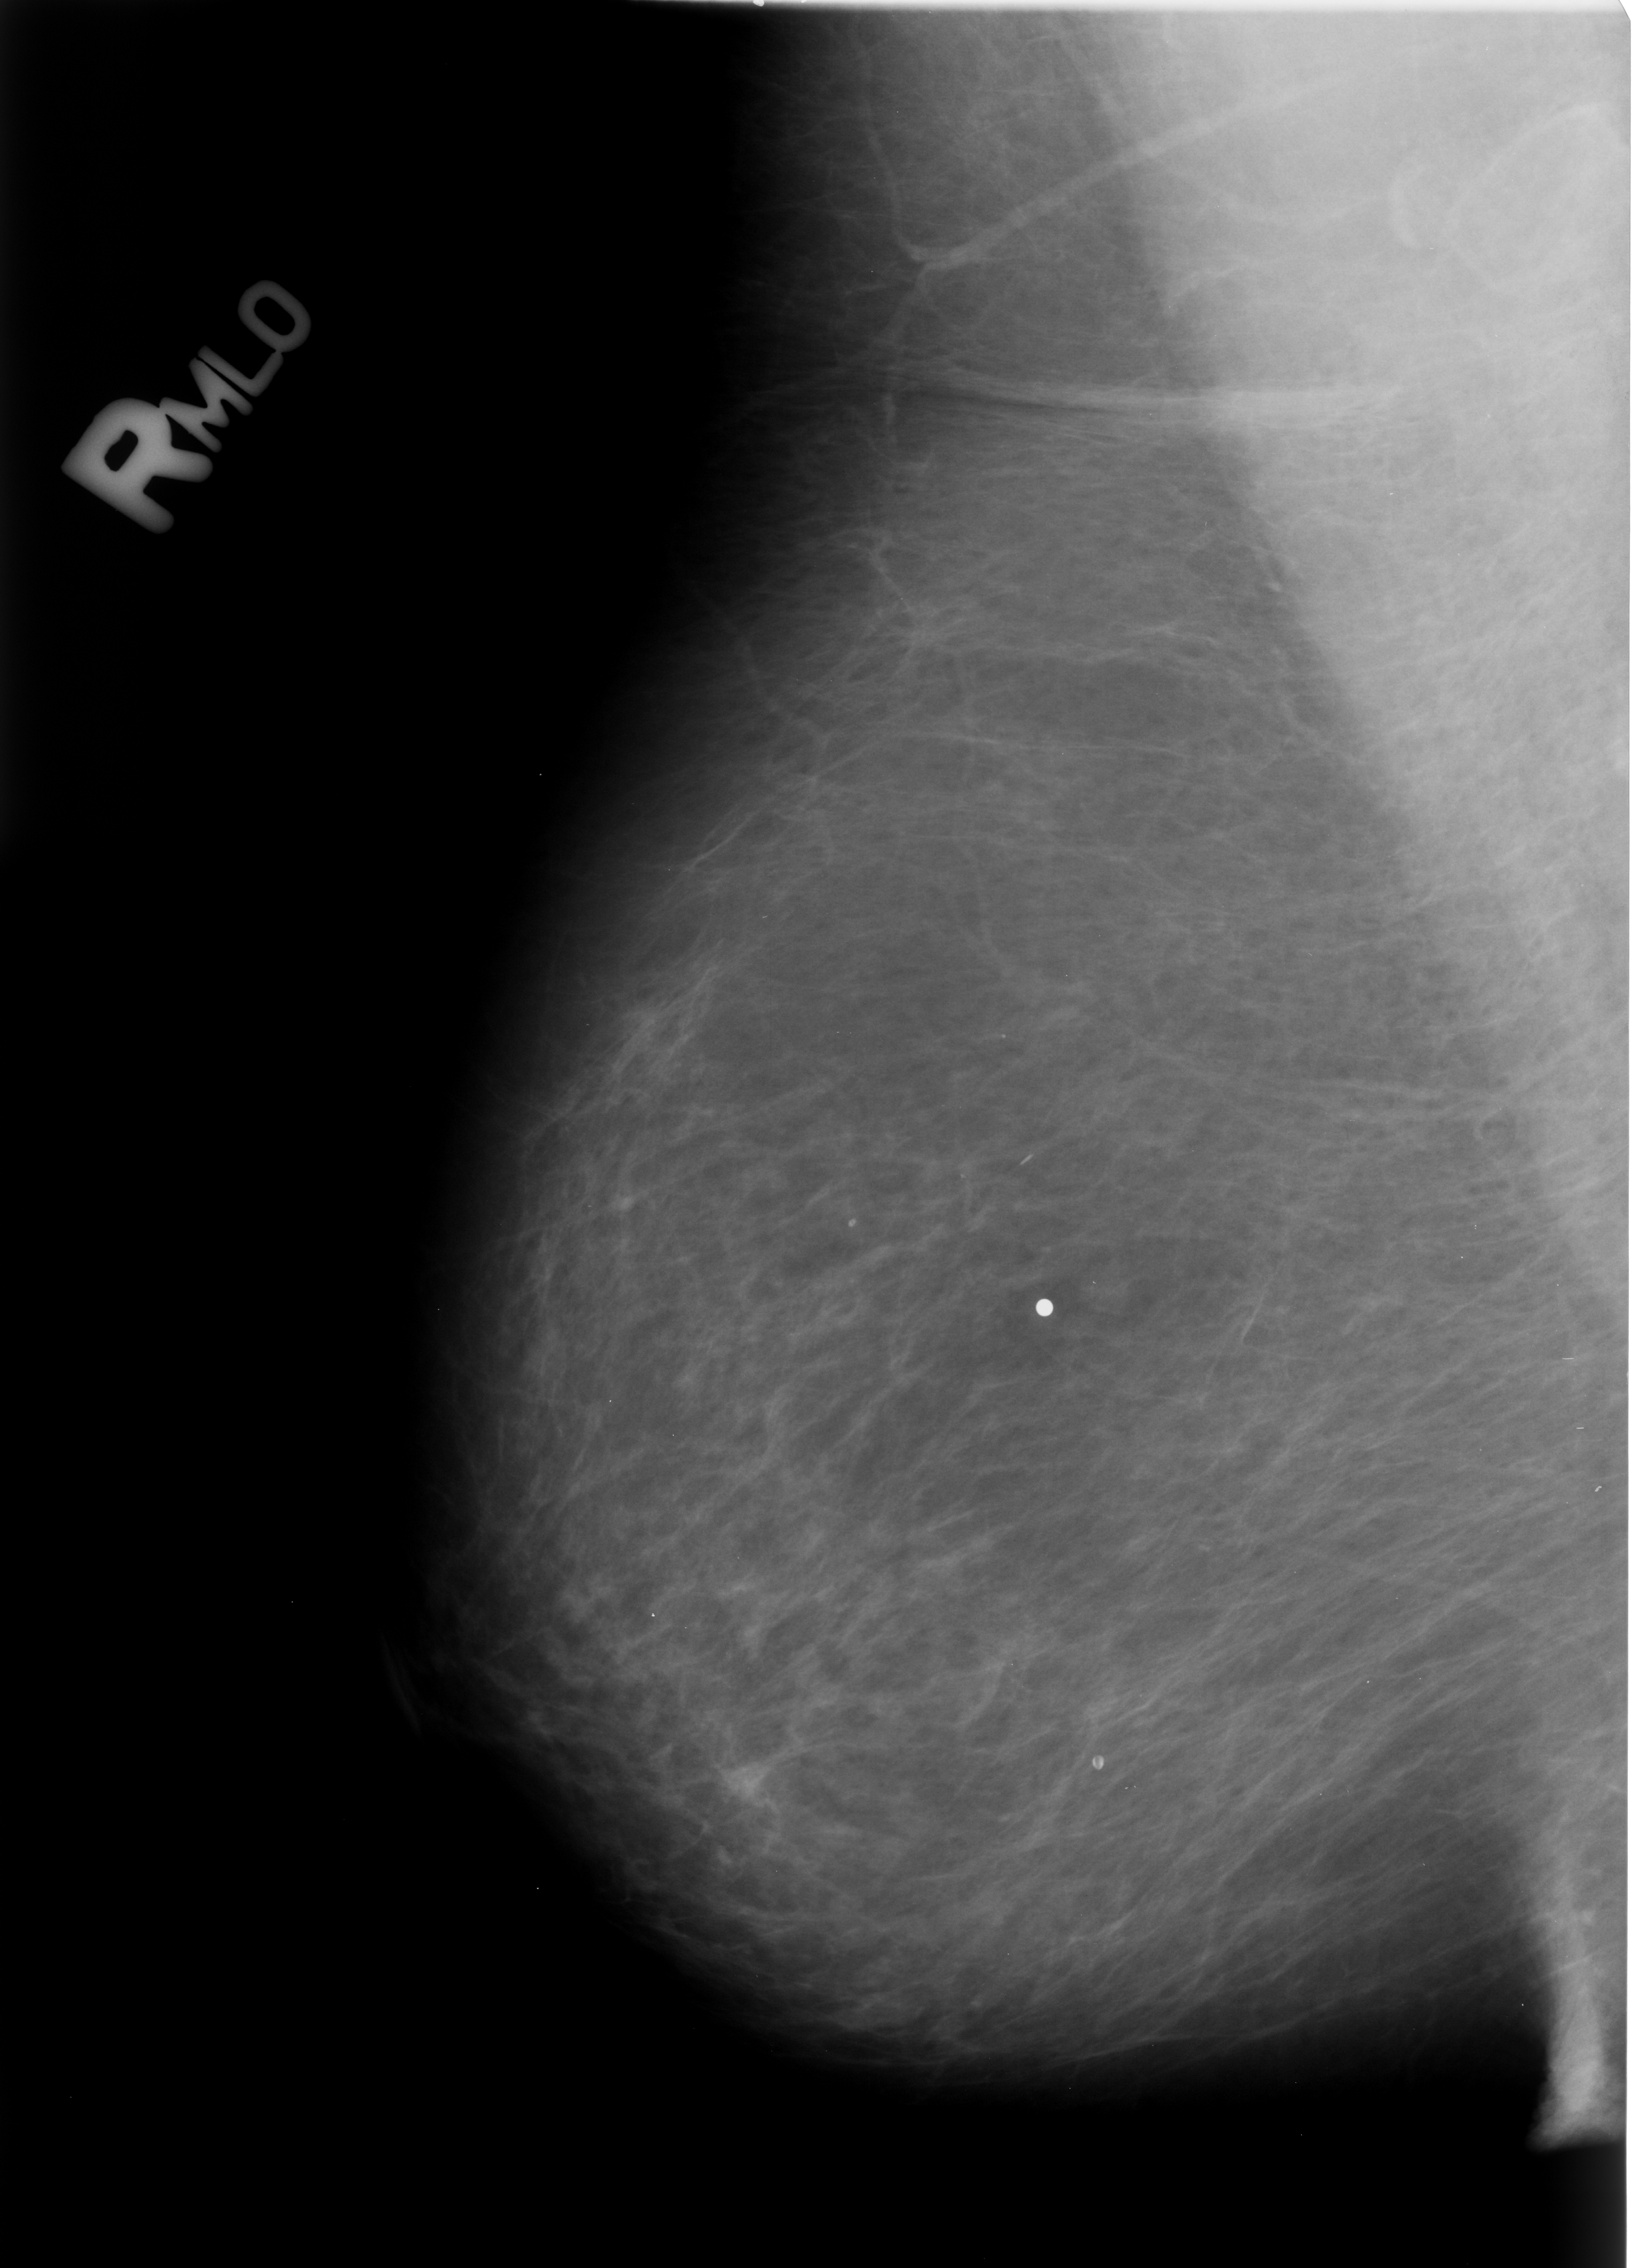
Mammogram (digitized film); right breast; mediolateral oblique (MLO) view; breast composition: almost entirely fatty (BI-RADS density category 1 of 4); 1635 × 2268 image matrix.
Expert-marked regions of interest on this film, with their recorded descriptors:
- Finding 1 of 2: calcifications, morphology lucent center; BI-RADS assessment category 2; subtlety rating 3 on a 1 (subtle) to 5 (obvious) scale; benign; no additional work-up was recommended (outcome (as recorded, no biopsy): benign without callback): bounding box <1015,1123,1059,1176> (left, top, right, bottom; pixels)
- Finding 2 of 2: calcifications, morphology lucent center; BI-RADS assessment category 2; outcome (as recorded, no biopsy): benign without callback (not worked up further): <1084,1747,1115,1778>